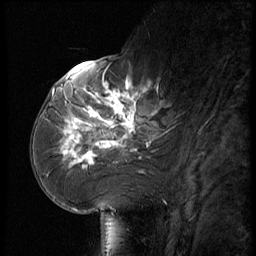
Breast MRI (dynamic contrast-enhanced), one sagittal slice; position 25 of 56 along the scan axis; dynamic contrast-enhanced series, image 2 of 3 at this slice position (ordered by acquisition); 1.5 T; TE 4.2 ms, TR 9 ms; 256 × 256 image matrix, field of view 180 × 180 mm. Patient: female, 61 years. From the clinical record (not read from this slice): setting: breast cancer imaged before/during neoadjuvant chemotherapy; receptor status: HR-positive, HER2-negative.
Annotated regions visible in this slice (semi-automatic segmentation, software-assisted and operator-edited):
- analysis volume of interest (the breast-tissue region the enhancement analysis was run in; not a lesion): bounding box [x1, y1, x2, y2] px = [65, 74, 185, 175]
- tumour enhancement mask (voxels above the 140 % enhancement threshold inside the analysis volume of interest): [65, 82, 149, 167]